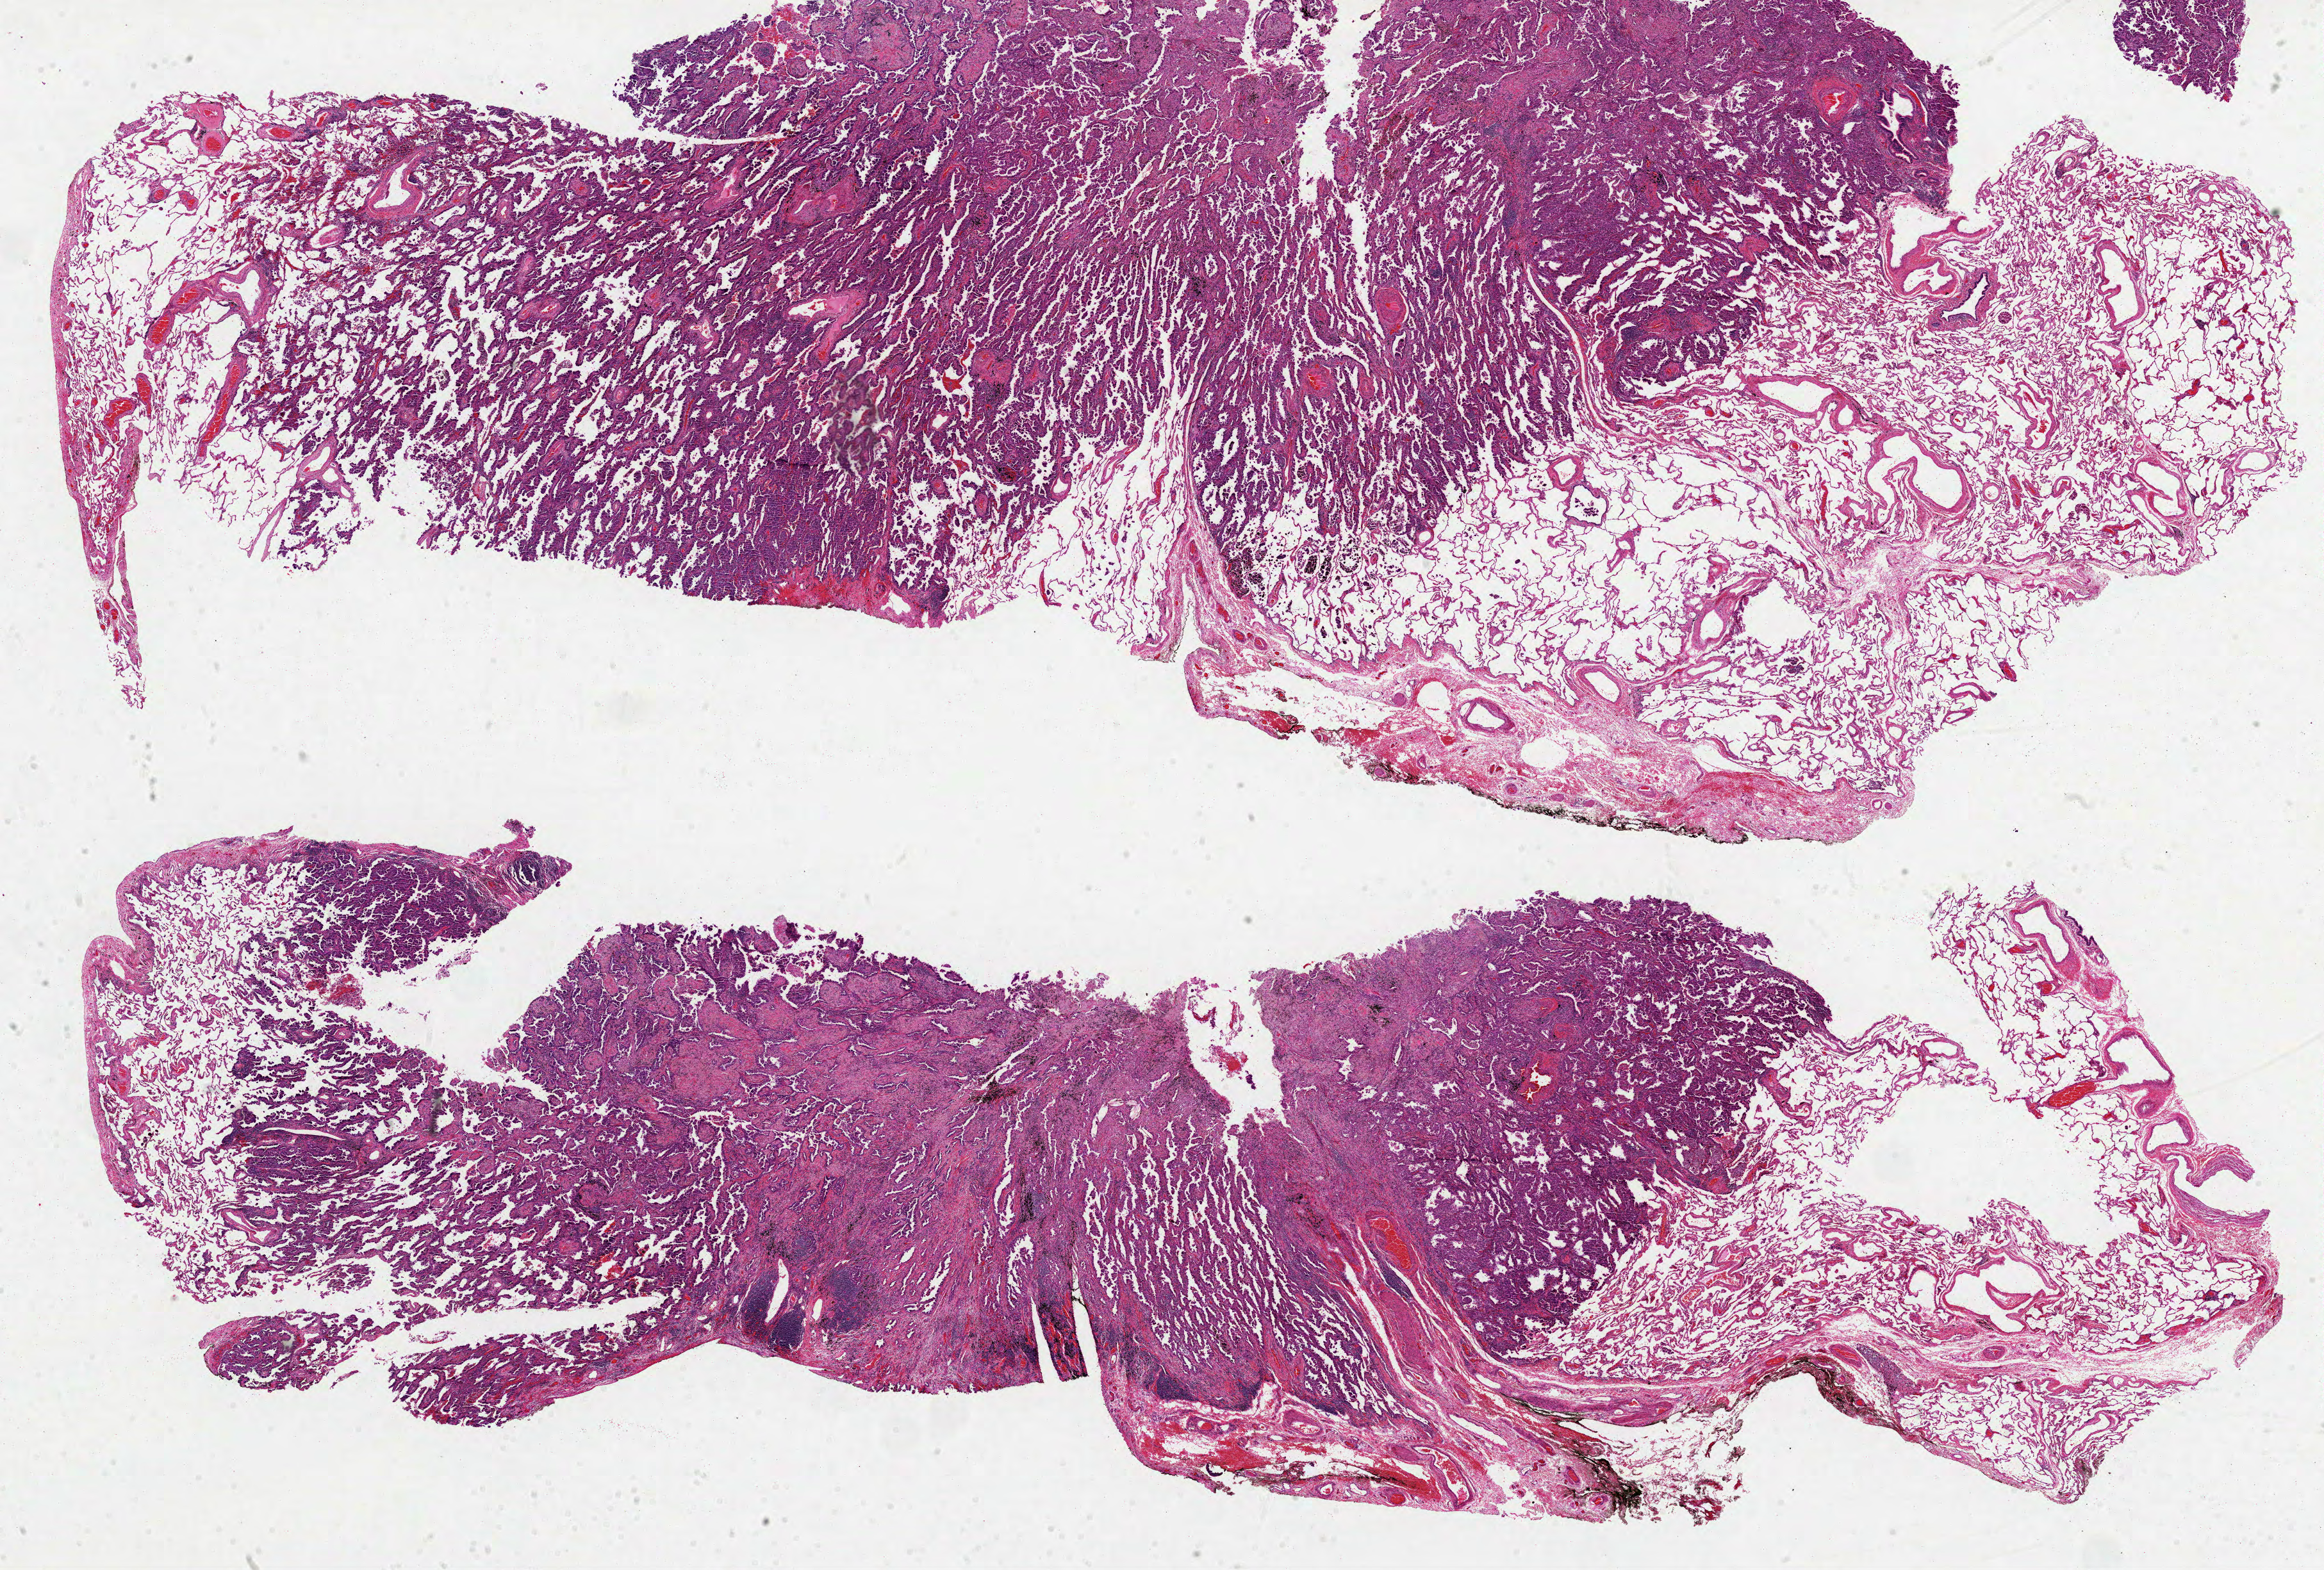
Whole-slide histology image, H&E-stained, shown as a low-resolution overview of the whole scanned area (about 29.2 x 19.8 mm). Formalin-fixed paraffin-embedded (FFPE) diagnostic section. Lung, primary tumour sample. Female patient; age at initial diagnosis 74 years.
- AJCC pathologic stage: IA (3rd edition)
- diagnosis: Adenocarcinoma, NOS (lower lobe, lung)
- laterality: left
- TNM: T1 N0 MX